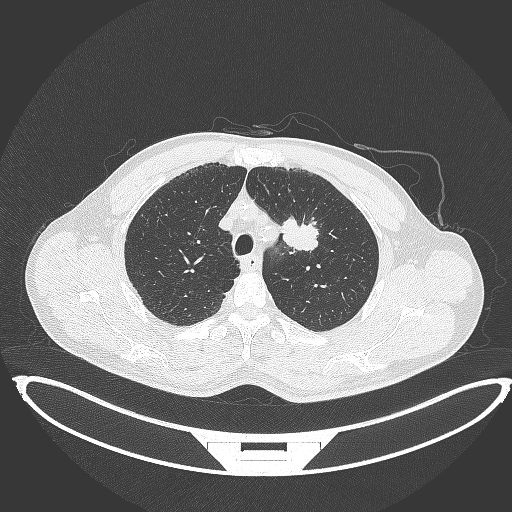
Chest CT, one axial slice; reconstruction kernel B70f; 120 kVp; lung window (W 1500 / L -600 HU); 1 mm slice thickness; 512 × 512 image matrix. Patient: male, 60 years. From the clinical record (not read from this slice): clinical TNM (as recorded): T2a N0 M0; histopathological grade: G1-G2.
Annotated regions visible in this slice (rectangle marked by the reading radiologist):
- lung tumour (recorded histology: squamous cell carcinoma): bounding box (x1, y1, x2, y2) in pixels: (280, 212, 322, 252)